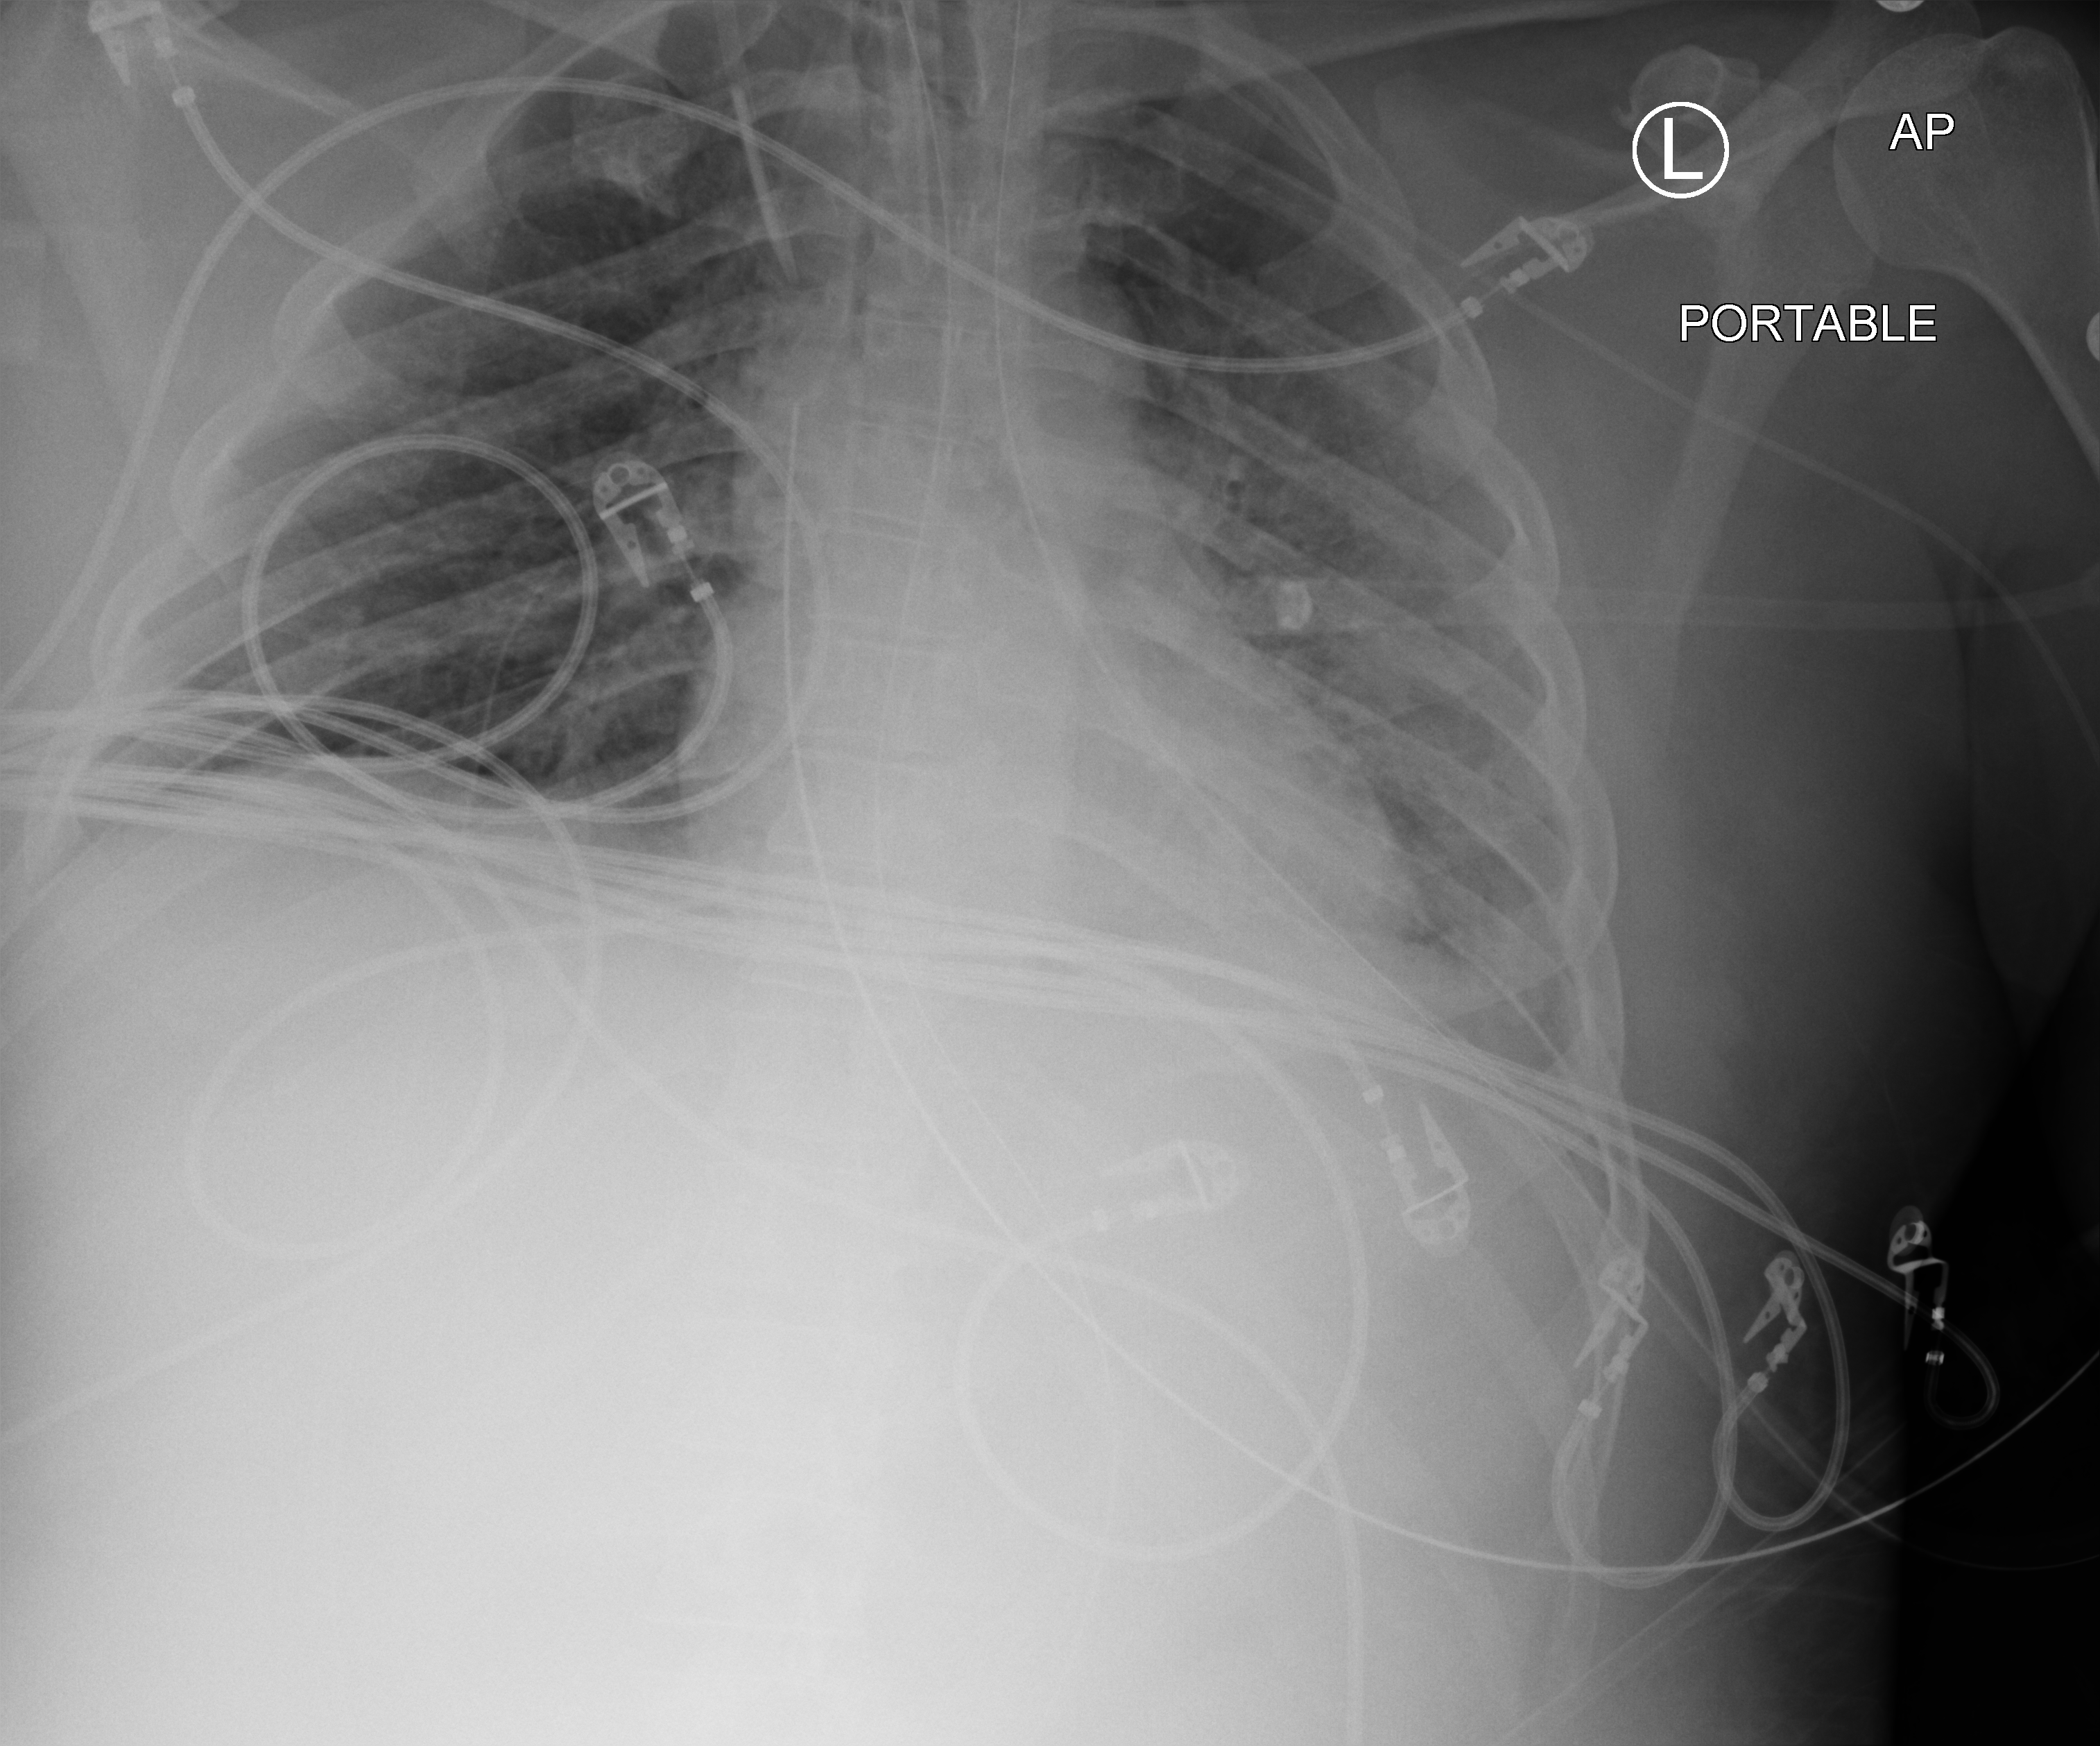
Portable chest radiograph; anteroposterior (AP) projection. Adult patient hospitalised with COVID-19, age 18–59 years.
Admission-level facts for this patient (not findings on this image; timing relative to this image not recorded):
- diabetes (admission record): no